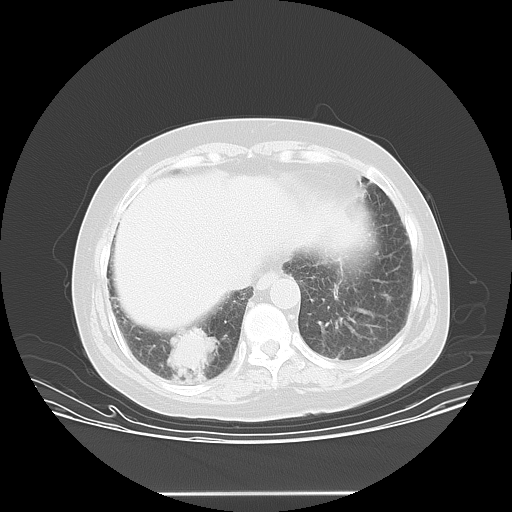
Chest CT, one axial slice; position 7 of 45 along the scan axis; reconstruction kernel LUNG; lung window (W 1500 / L -600 HU); 512 × 512 image matrix. Patient: female, 55 years. Case-level facts recorded for this patient, not image findings: clinical TNM (as recorded): T2 N0 M1b.
Outlined on this slice (rectangle marked by the reading radiologist):
- lung tumour (recorded histology: squamous cell carcinoma): bounding box (x1, y1, x2, y2) in pixels: (152, 323, 222, 392)